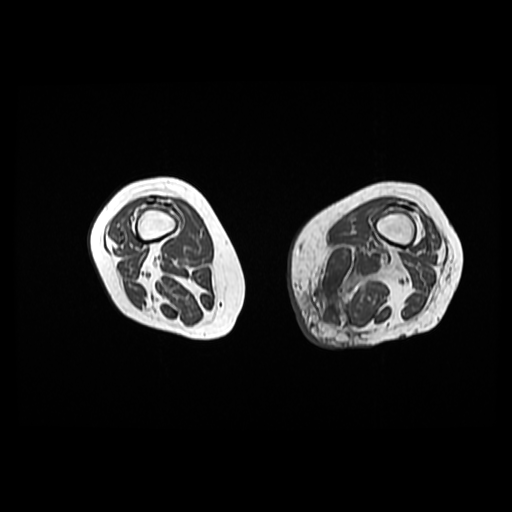
MRI of an extremity soft-tissue mass, one axial slice. Position 21 of 42 along the scan axis. 6 mm slice thickness. 512 × 512 image matrix, field of view 420 × 420 mm. Female patient. Case-level facts recorded for this patient, not image findings: histological type: pleomorphic leiomyosarcoma; grade: high; site of the primary tumour: left thigh.
Annotated regions visible in this slice (expert manual segmentation):
- gross tumour volume including surrounding oedema: bounding box [x1, y1, x2, y2] px = [307, 244, 404, 328]